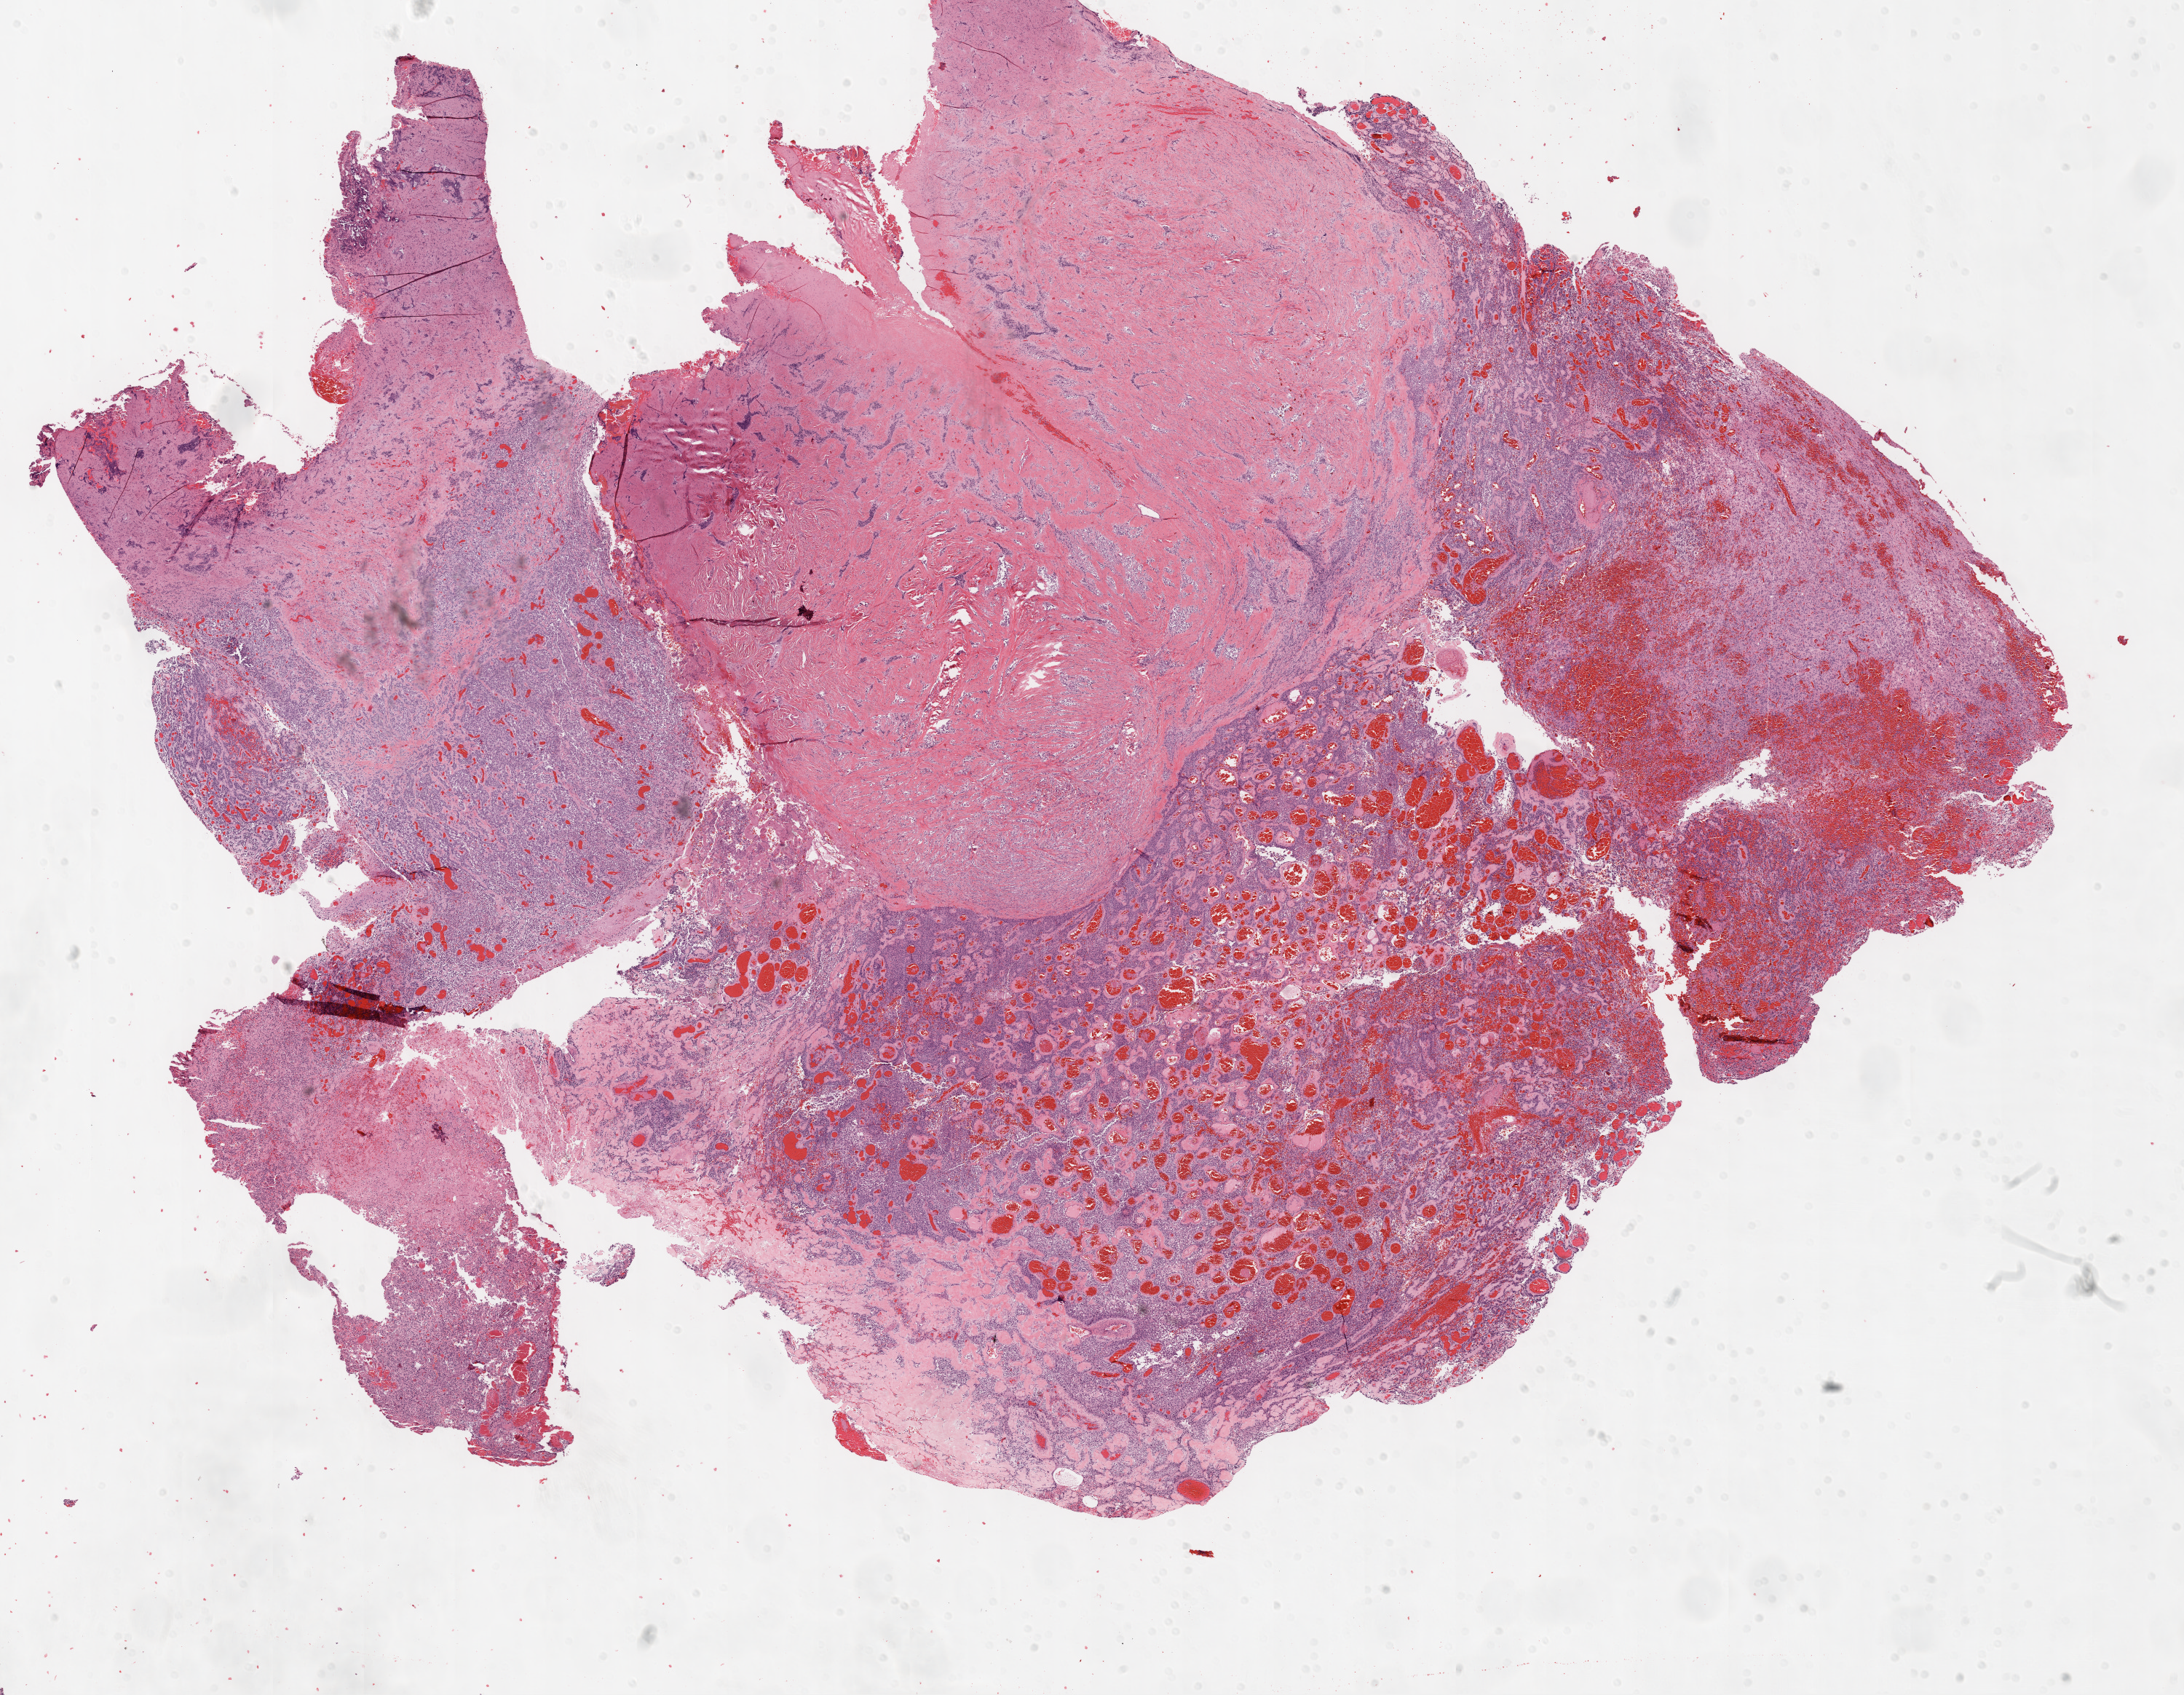
H&E whole-slide image, shown as a low-resolution overview of the whole scanned area (about 24.1 x 18.7 mm). Formalin-fixed paraffin-embedded (FFPE) diagnostic section. Brain, primary tumour sample. Female patient; age at initial diagnosis 36 years.
Pathologic diagnosis: Glioblastoma.